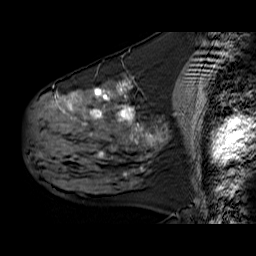
Breast MRI (dynamic contrast-enhanced), one sagittal slice. Slice 29 of 60 in the series (ordered by position). Dynamic contrast-enhanced series, time point 2 of 6 at this slice position (early post-contrast). 1.5 T. TE 6.3 ms, TR 32.9 ms. 4 mm slice thickness. 256 × 256 image matrix, field of view 200 × 200 mm. Female patient. Case-level facts recorded for this patient, not image findings: setting: breast cancer imaged before/during neoadjuvant chemotherapy; receptor status: HER2-positive.
Annotated regions visible in this slice (semi-automatic segmentation, software-assisted and operator-edited):
- analysis volume of interest (the breast-tissue region the enhancement analysis was run in; not a lesion): box from (x=30, y=79) to (x=165, y=180) px
- tumour enhancement mask (voxels above the 100 % enhancement threshold inside the analysis volume of interest): (x=55, y=82)–(x=159, y=171)